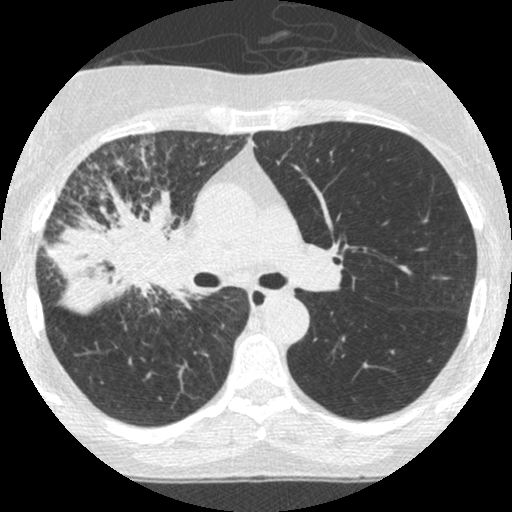
Low-dose screening chest CT, one axial slice; position 160 of 253 along the scan axis; reconstruction kernel STANDARD; 120 kVp; lung window (W 1500 / L -600 HU); 512 × 512 image matrix, field of view 294 × 294 mm.
Annotated regions visible in this slice (expert manual segmentation):
- lesion 2 (tumor, hilum of right lung): box from (x=46, y=189) to (x=184, y=316) px